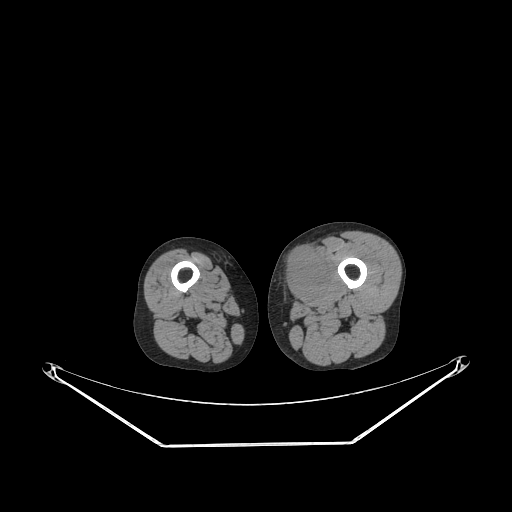
CT of an extremity soft-tissue mass (from a PET/CT study), one axial slice. Slice 218 of 267 in the series (ordered by position). 140 kVp. Soft-tissue window (W 400 / L 40 HU). 512 × 512 image matrix. Male patient. From the clinical record (not read from this slice): histological type: pleiomorphic leiomyosarcoma; grade: high; site of the primary tumour: left thigh.
Structures marked on this image (expert contour drawn on MRI and transferred to this co-registered scan by the dataset authors):
- gross tumour volume including surrounding oedema: bounding box (x1, y1, x2, y2) in pixels: (281, 249, 330, 300)
- gross tumour volume (mass): (281, 249, 325, 300)